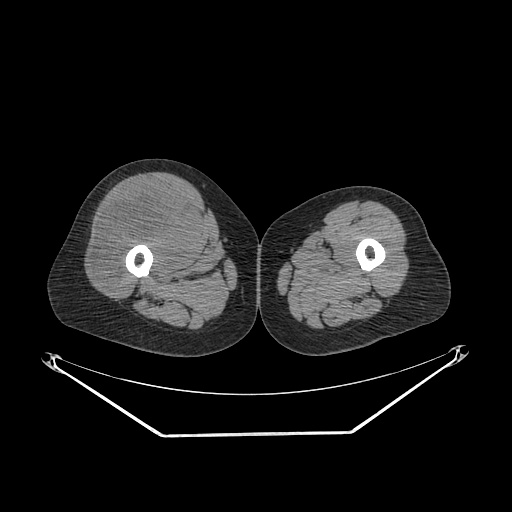
CT of an extremity soft-tissue mass (from a PET/CT study), one axial slice; slice 246 of 311 in the series (ordered by position); reconstruction kernel SOFT; 140 kVp; soft-tissue window (W 400 / L 40 HU); 512 × 512 image matrix. Female patient. Case-level facts recorded for this patient, not image findings: histological type: pleiomorphic undifferentiated sarcoma; grade: high; site of the primary tumour: right quadricep.
Annotated regions visible in this slice (expert contour drawn on MRI and transferred to this co-registered scan by the dataset authors):
- tumour plus oedema (research contour): bounding box (x1, y1, x2, y2) in pixels: (96, 185, 197, 286)
- tumour (research contour): (96, 185, 197, 286)